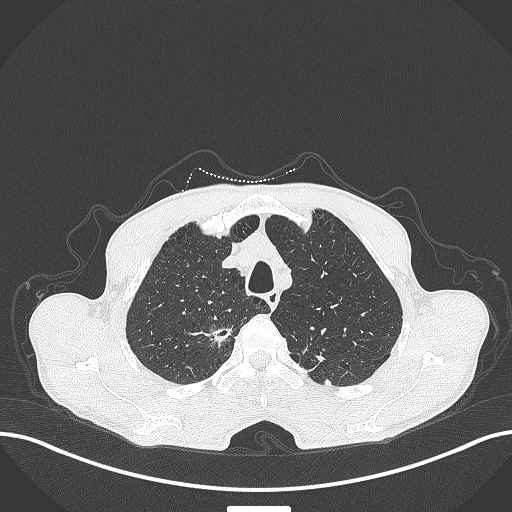
Chest CT, one axial slice; position 354 of 445 along the scan axis; reconstruction kernel B70f; 120 kVp; lung window (W 1500 / L -600 HU); 1 mm slice thickness; 512 × 512 image matrix. Patient: male, 70 years. Case-level facts recorded for this patient, not image findings: clinical TNM (as recorded): T1a N0 M0.
Outlined on this slice (rectangle marked by the reading radiologist):
- lung tumour (recorded histology: adenocarcinoma): box from (x=202, y=318) to (x=233, y=350) px